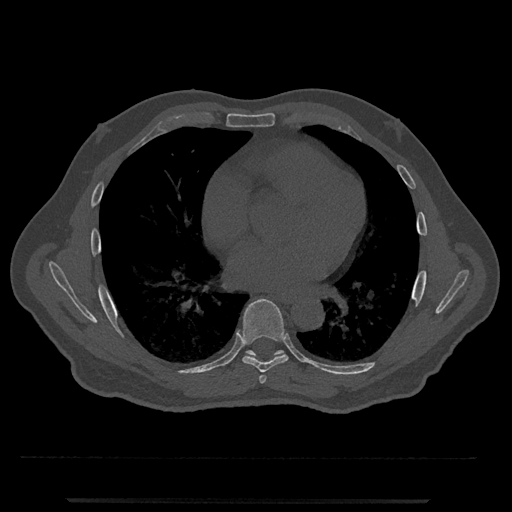
CT including the spine, one axial slice. Slice 672 of 797 in the series (ordered by position). Reconstruction kernel Br40s/3. 120 kVp. Bone window (W 1800 / L 400 HU). 0.5 mm slice thickness. 512 × 512 image matrix, field of view 419 × 419 mm. Male patient, age 63 years. Case-level facts recorded for this patient, not image findings: primary cancer: prostate.
Annotated regions visible in this slice (semi-automatic segmentation, software-assisted and operator-edited):
- T6 vertebra: bounding box [x1, y1, x2, y2] px = [259, 375, 267, 384]
- T7 vertebra: [236, 298, 289, 373]
- T8 vertebra: [246, 350, 284, 356]